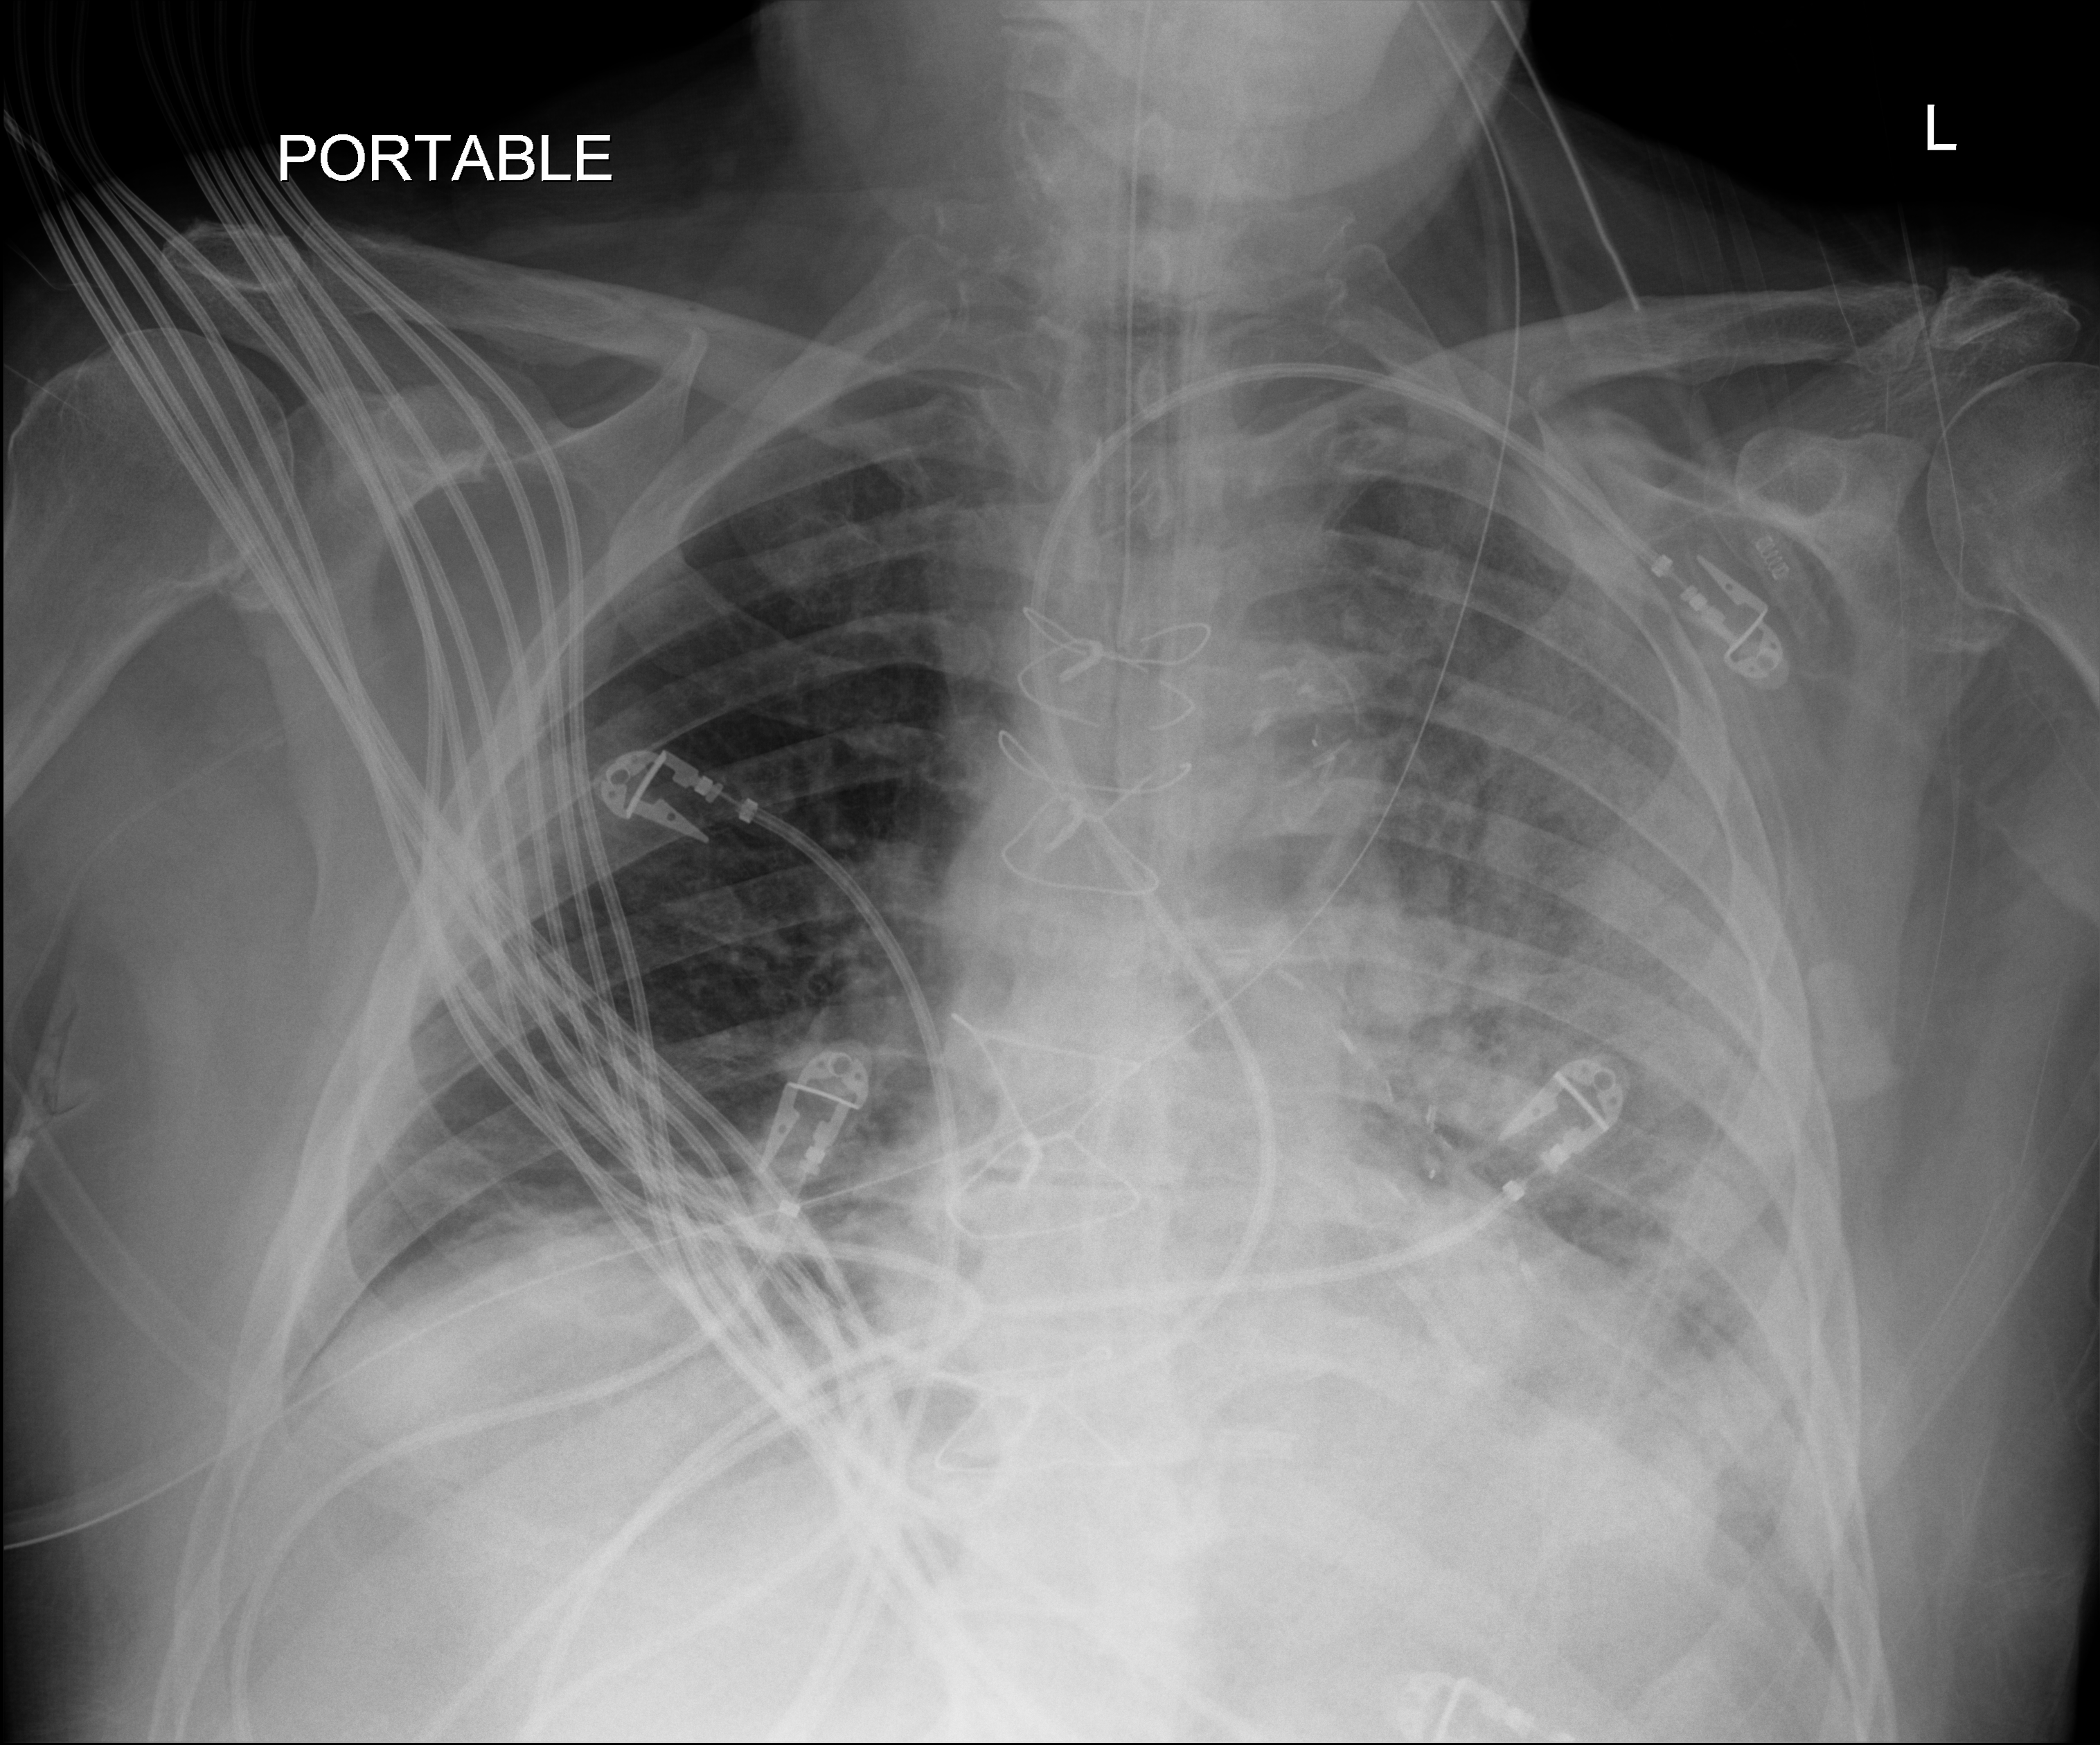
Portable chest radiograph; anteroposterior (AP) projection. Male patient hospitalised with COVID-19, age 60–74 years.
Hospital-stay facts (about this admission, not read from this image; timing relative to this image not recorded):
- smoking status (admission record): former
- admitted to intensive care during this hospital stay: yes